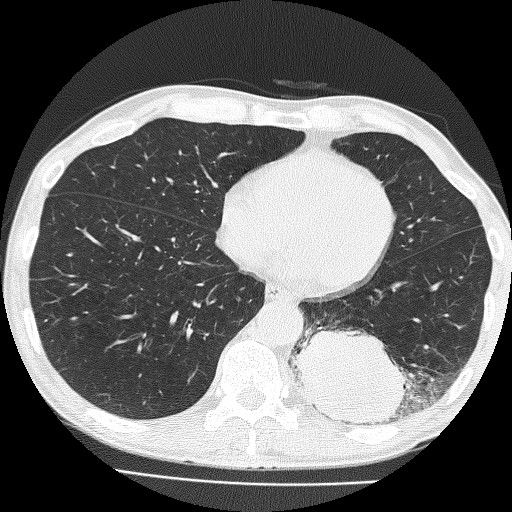
Low-dose screening chest CT, one axial slice. Slice 59 of 160 in the series (ordered by position). 120 kVp. Lung window (W 1500 / L -600 HU). 2 mm slice thickness. 512 × 512 image matrix, field of view 324 × 324 mm.
Structures marked on this image (outlined manually by an expert reader):
- lesion 1 (tumor, lower lobe of left lung): bounding box <294,329,409,426> (left, top, right, bottom; pixels)